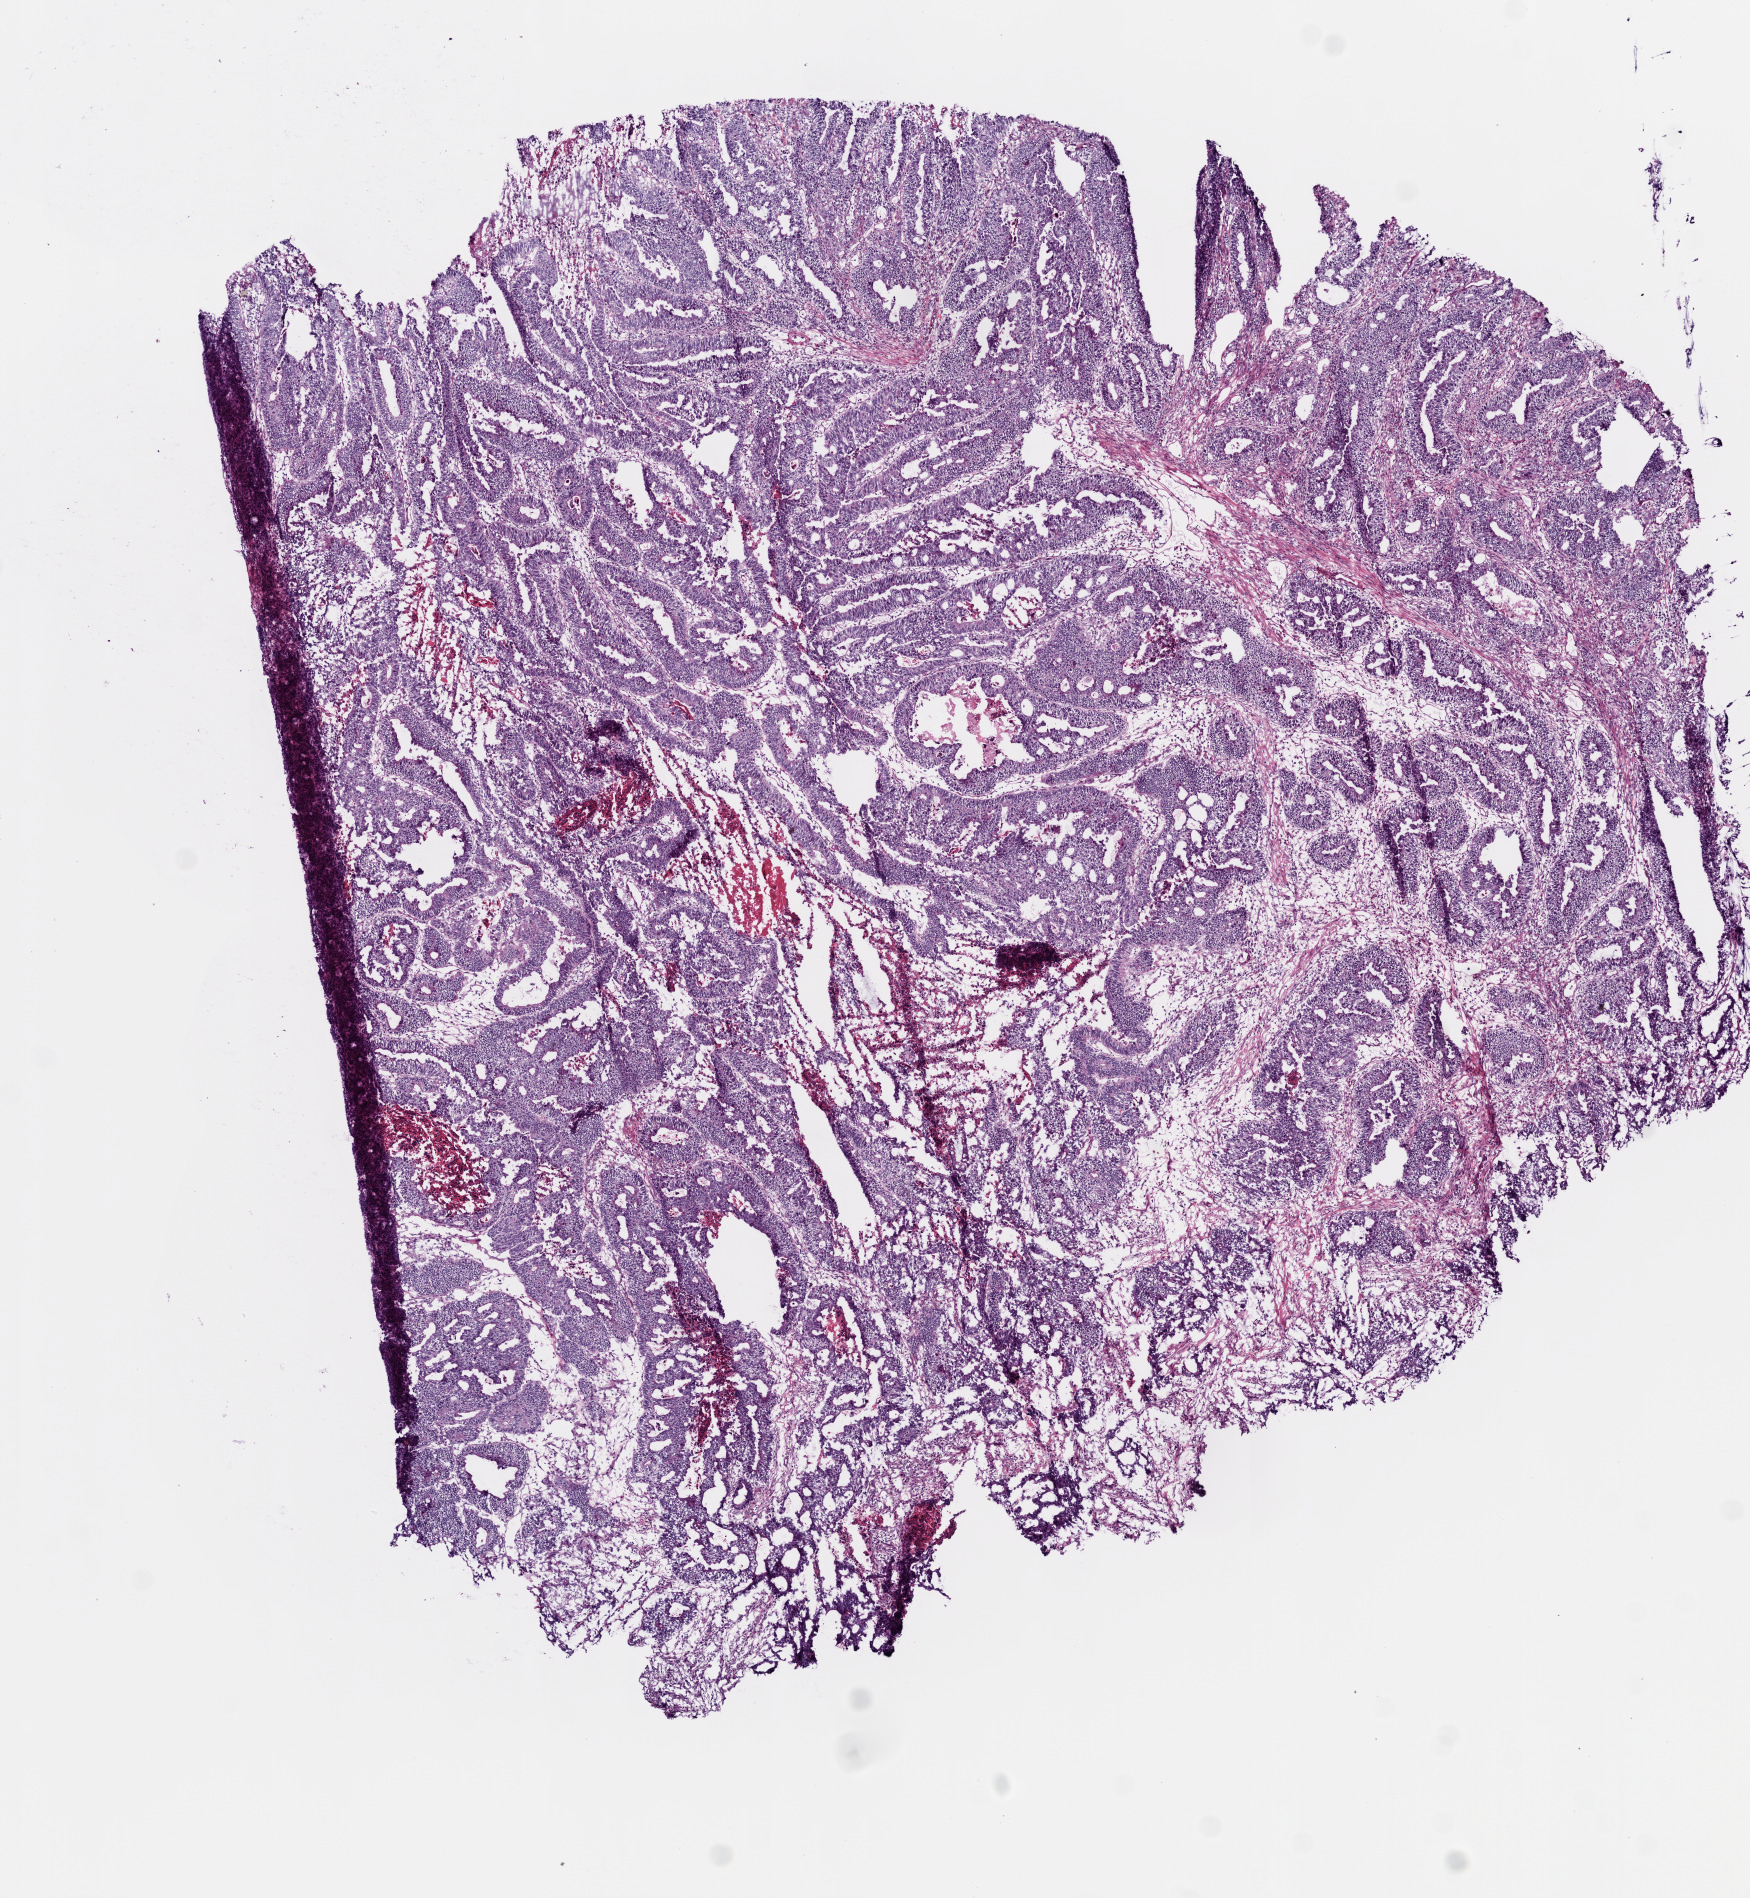
Hematoxylin and eosin (H&E) stained whole-slide image, whole scanned area (about 7.0 x 7.6 mm, from a 20x scan) shown as a low-resolution overview. Frozen section from the top of the tissue portion. Sample: primary tumour, colon. Male, age 80 years at initial diagnosis. Slide review estimates, as recorded: tumour cells 80%, tumour nuclei 75%, normal cells 0%, stromal cells 10%, necrosis 10%.
Diagnosis: Adenocarcinoma, NOS. AJCC pathologic stage: IV. TNM: T3 N1 M1.